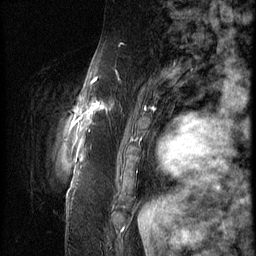
Breast MRI (dynamic contrast-enhanced), one sagittal slice. Slice 13 of 66 in the series (ordered by position). 3 images stored at this slice position (order not interpretable as contrast timing). 1.5 T. TE 4.2 ms, TR 9 ms. 256 × 256 image matrix, field of view 180 × 180 mm. Female patient, age 57 years. Case-level facts recorded for this patient, not image findings: setting: breast cancer imaged before/during neoadjuvant chemotherapy; receptor status: triple-negative.
Annotated regions visible in this slice (semi-automatically segmented with operator editing):
- analysis volume of interest (the breast-tissue region the enhancement analysis was run in; not a lesion): box from (x=86, y=74) to (x=138, y=129) px
- tumour enhancement mask (voxels above the 140 % enhancement threshold inside the analysis volume of interest): (x=86, y=78)–(x=107, y=129)